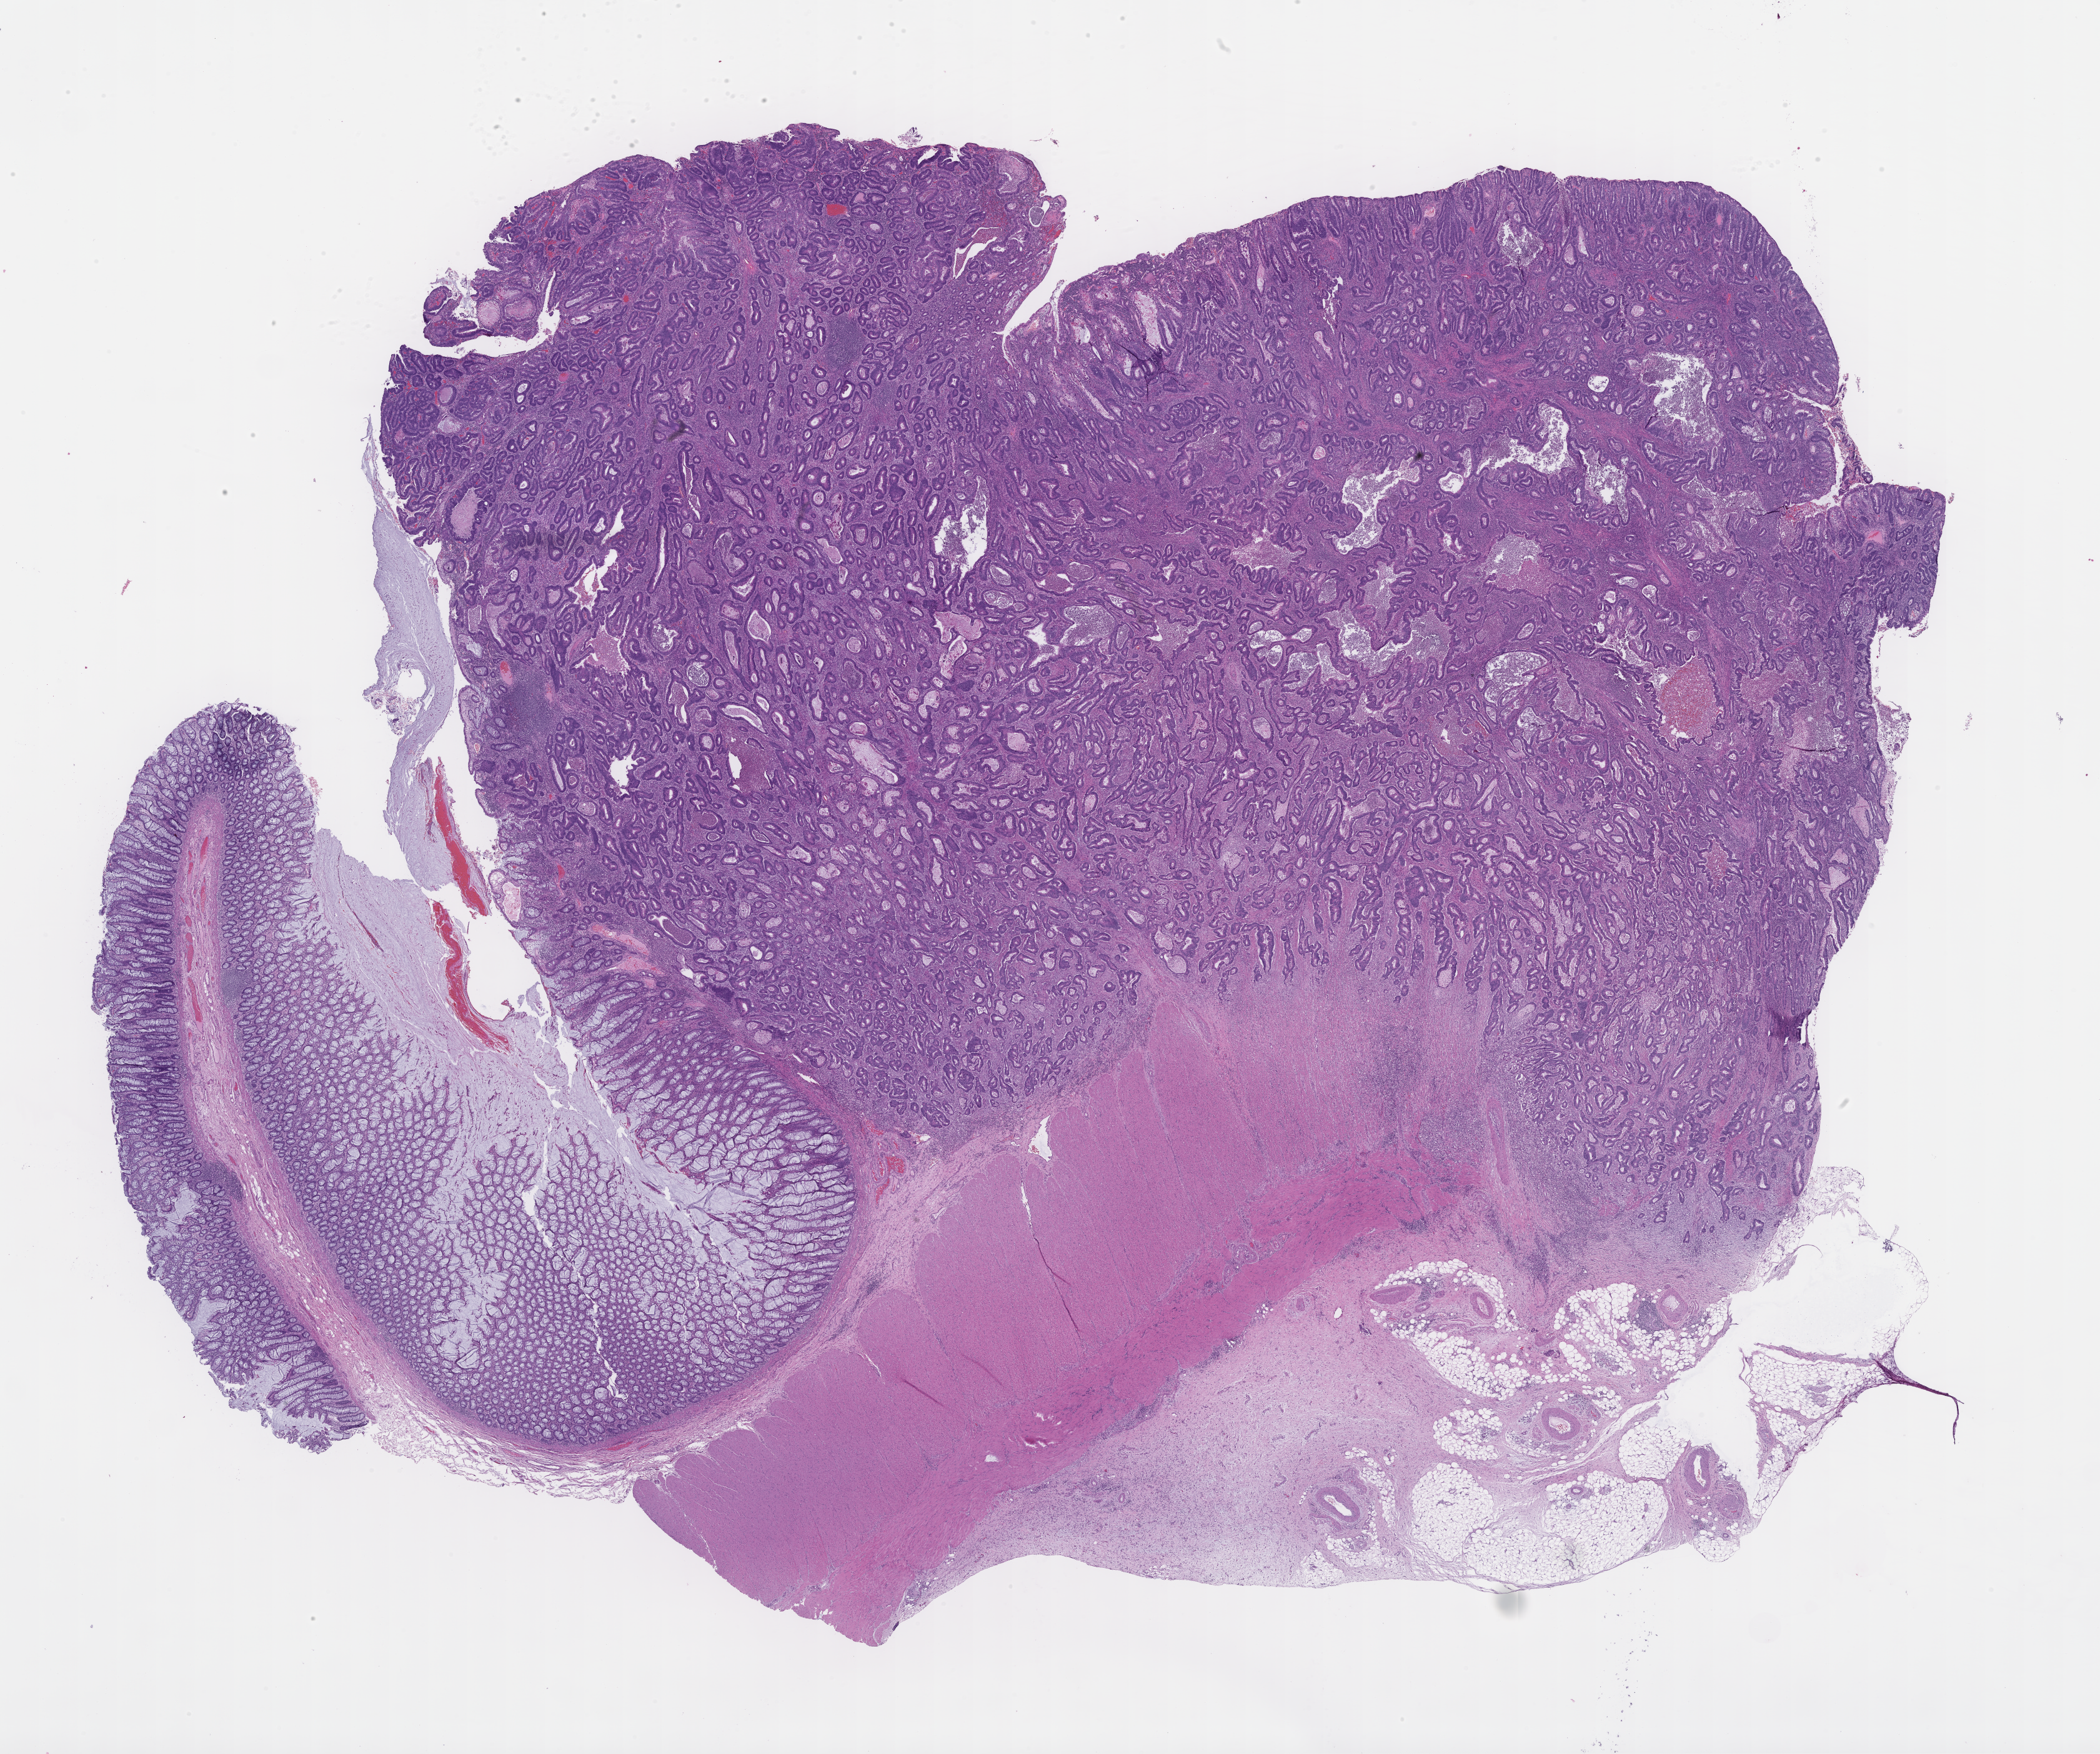
Whole-slide image, hematoxylin and eosin (H&E) stain — whole scanned area (about 27.1 x 22.7 mm) shown as a low-resolution overview, formalin-fixed paraffin-embedded section, site: colon. Patient: female.
This section: primary tumour tissue. Diagnosis: Colorectal Carcinoma.